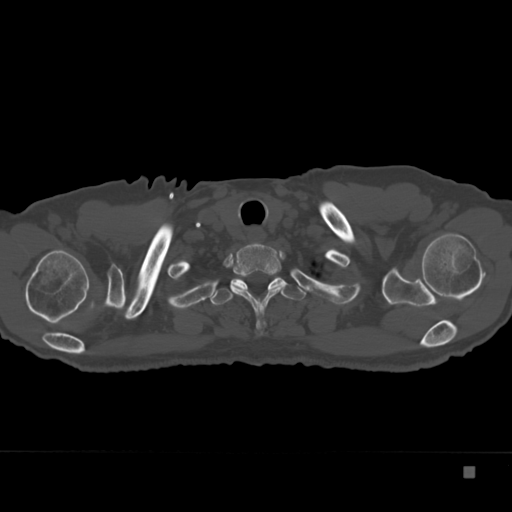
CT including the spine, one axial slice; slice 309 of 332 in the series (ordered by position); reconstruction kernel Br40s; 120 kVp; bone window (W 1800 / L 400 HU); 512 × 512 image matrix, field of view 389 × 389 mm. Male patient, age 72 years. Case-level facts recorded for this patient, not image findings: primary cancer: skeletal.
Annotated regions visible in this slice (semi-automatic segmentation, software-assisted and operator-edited):
- T1 vertebra: bounding box [x1, y1, x2, y2] px = [231, 242, 281, 328]
- T2 vertebra: [211, 274, 306, 306]